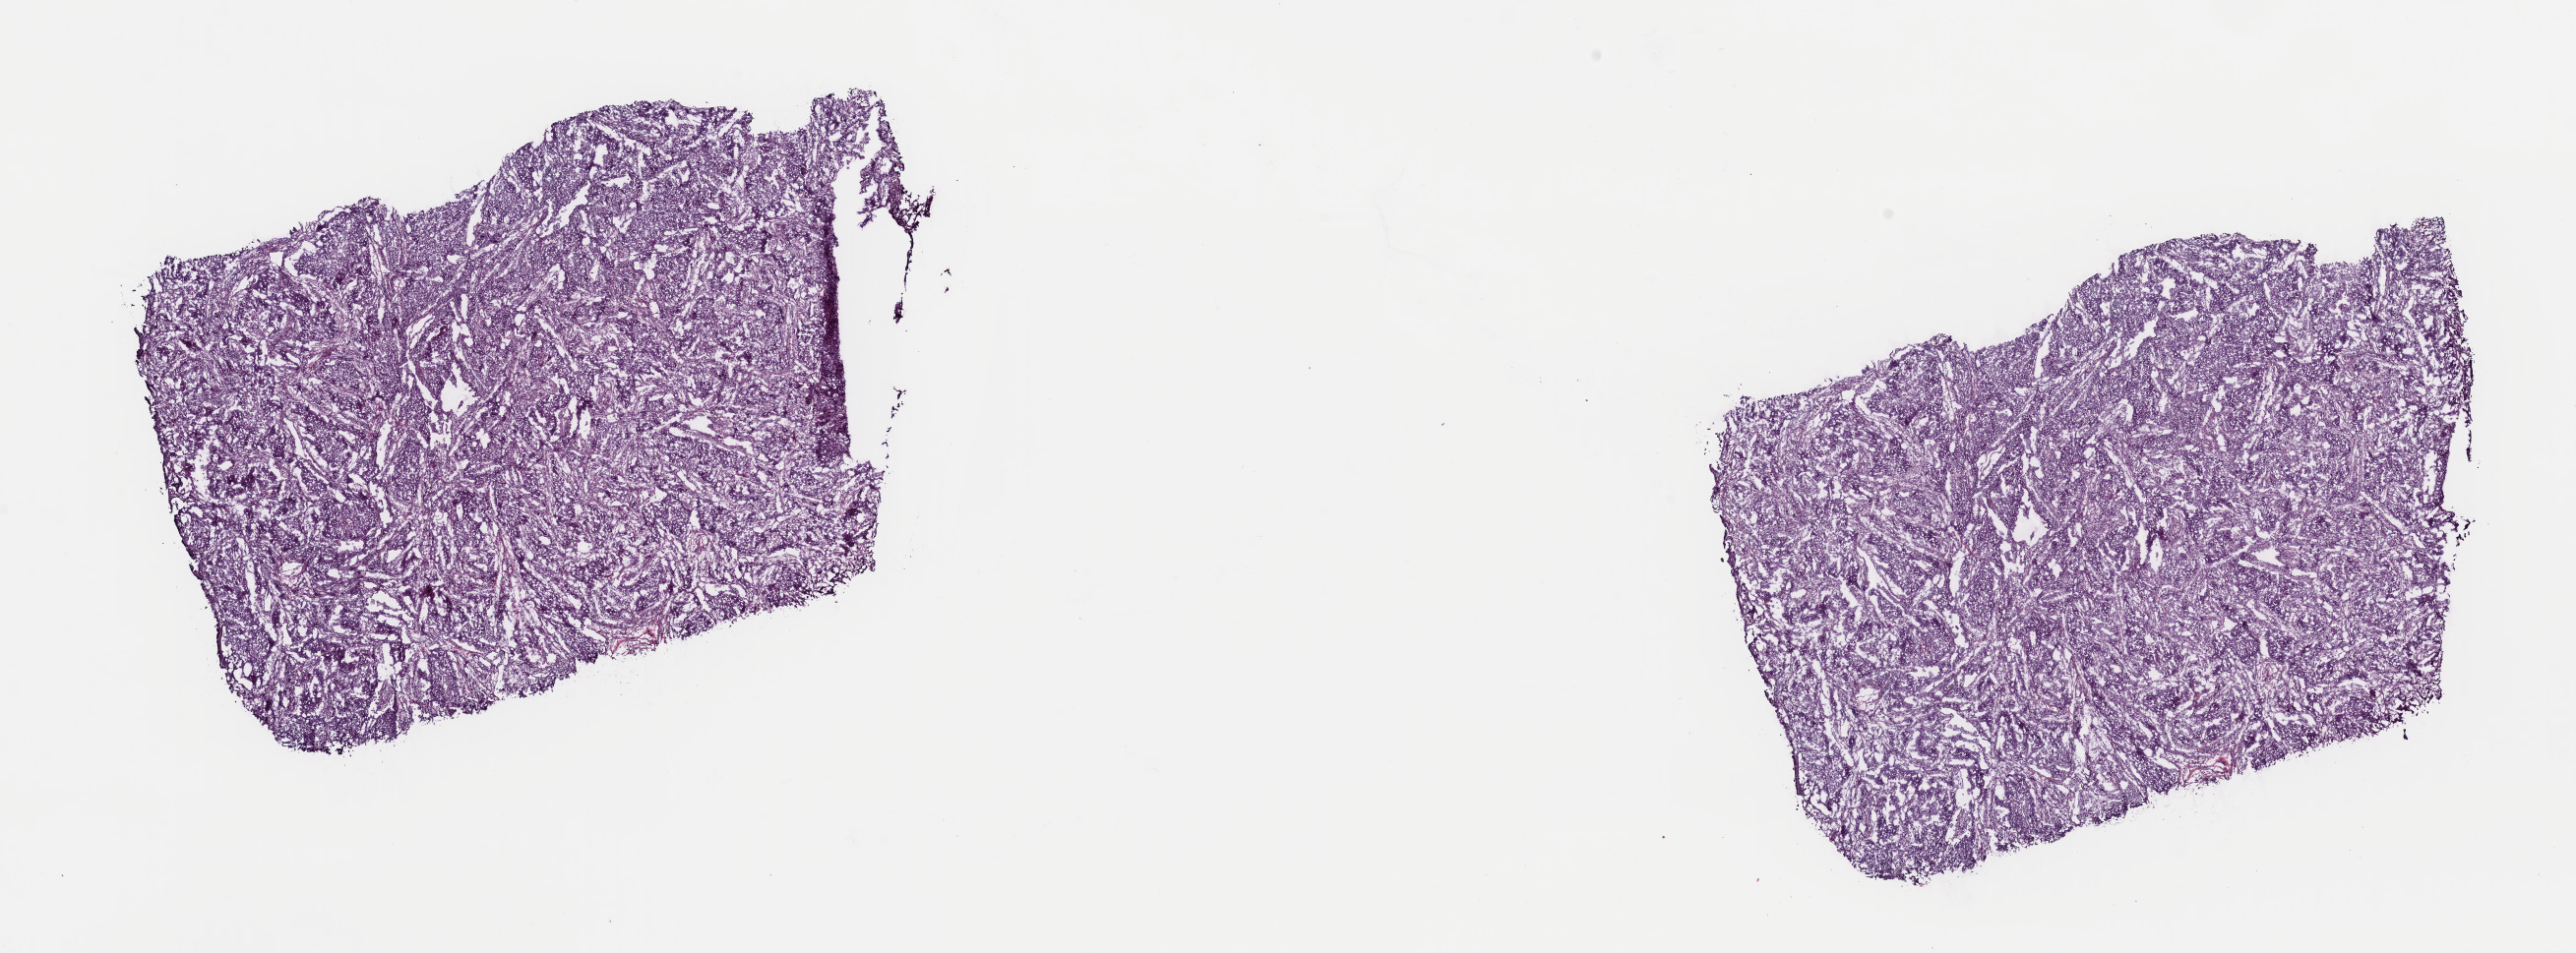
H&E-stained whole-slide image — low-resolution overview of the scanned area, about 20.7 x 7.7 mm, frozen section, sample: primary tumour, lung. Patient: female, age at initial diagnosis 62 years. Slide review estimates, as recorded: tumour cells 100%, tumour nuclei 75%, normal cells 0%, stromal cells 0%, necrosis 0%. Infiltration values recorded for this section: lymphocyte infiltration 5%, monocyte infiltration 0%, neutrophil infiltration 0%.
AJCC pathologic stage: IIA. Histologic diagnosis: Adenocarcinoma, NOS.